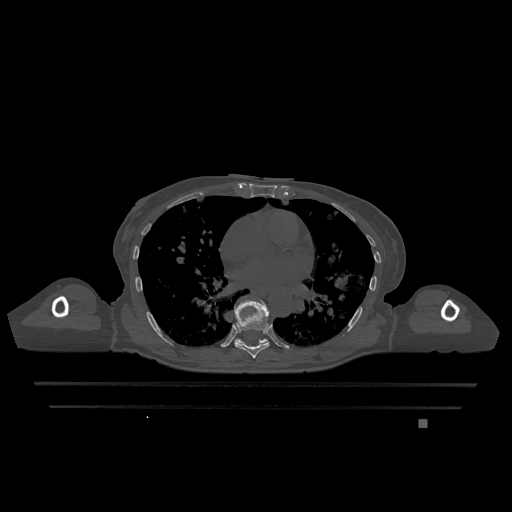
CT including the spine, one axial slice. Slice 726 of 1317 in the series (ordered by position). Bone window (W 1800 / L 400 HU). 0.5 mm slice thickness. 512 × 512 image matrix, field of view 500 × 500 mm. Patient: female, 74 years. From the clinical record (not read from this slice): primary cancer: lung.
Structures marked on this image (semi-automatic segmentation, software-assisted and operator-edited):
- T7 vertebra: box from (x=235, y=300) to (x=270, y=358) px
- T9 vertebra: (x=235, y=338)–(x=268, y=345)